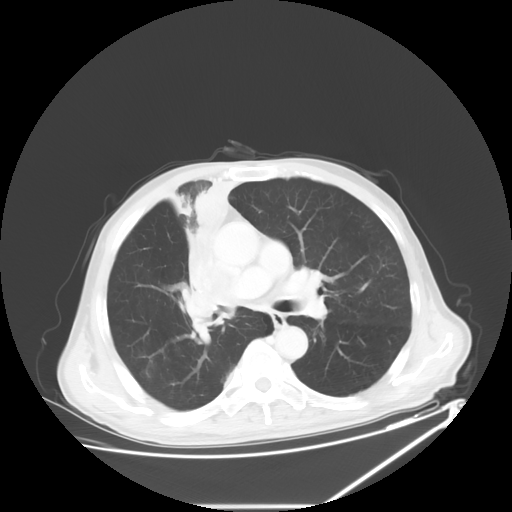
Chest CT, one axial slice. Lung window (W 1500 / L -600 HU). 5 mm slice thickness. 512 × 512 image matrix, field of view 410 × 410 mm. Male patient, age 73 years. From the clinical record (not read from this slice): clinical TNM (as recorded): T2a N1 M0.
Outlined on this slice (rectangle marked by the reading radiologist):
- lung tumour (recorded histology: squamous cell carcinoma): box from (x=182, y=172) to (x=249, y=339) px